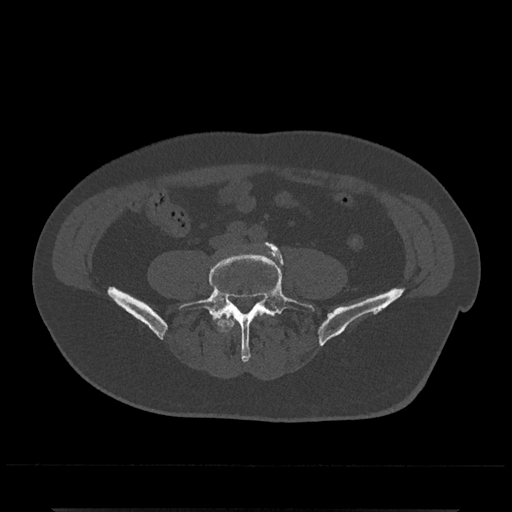
CT including the spine, one axial slice; slice 100 of 797 in the series (ordered by position); reconstruction kernel Br40s/3; 120 kVp; bone window (W 1800 / L 400 HU); 512 × 512 image matrix. Male patient, age 67 years. From the clinical record (not read from this slice): primary cancer: prostate.
Outlined on this slice (semi-automatically segmented with operator editing):
- L4 vertebra: bounding box (x1, y1, x2, y2) in pixels: (219, 312, 265, 332)
- L5 vertebra: (179, 242, 315, 362)